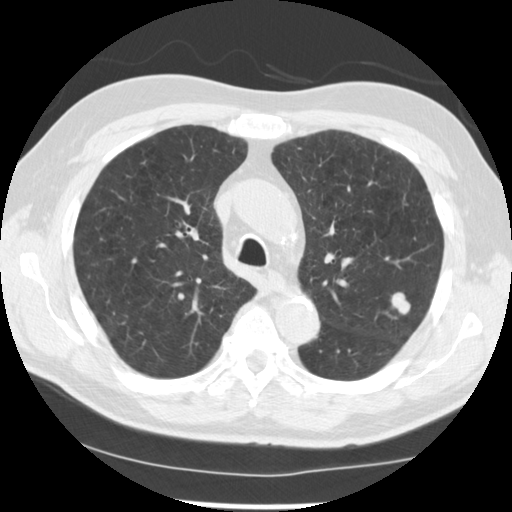
Low-dose screening chest CT, one axial slice. Position 172 of 249 along the scan axis. 120 kVp. Lung window (W 1500 / L -600 HU). 2.5 mm slice thickness. 512 × 512 image matrix, field of view 341 × 341 mm.
Structures marked on this image (expert manual segmentation):
- lesion 1 (tumor, upper lobe of left lung): box from (x=391, y=292) to (x=410, y=314) px